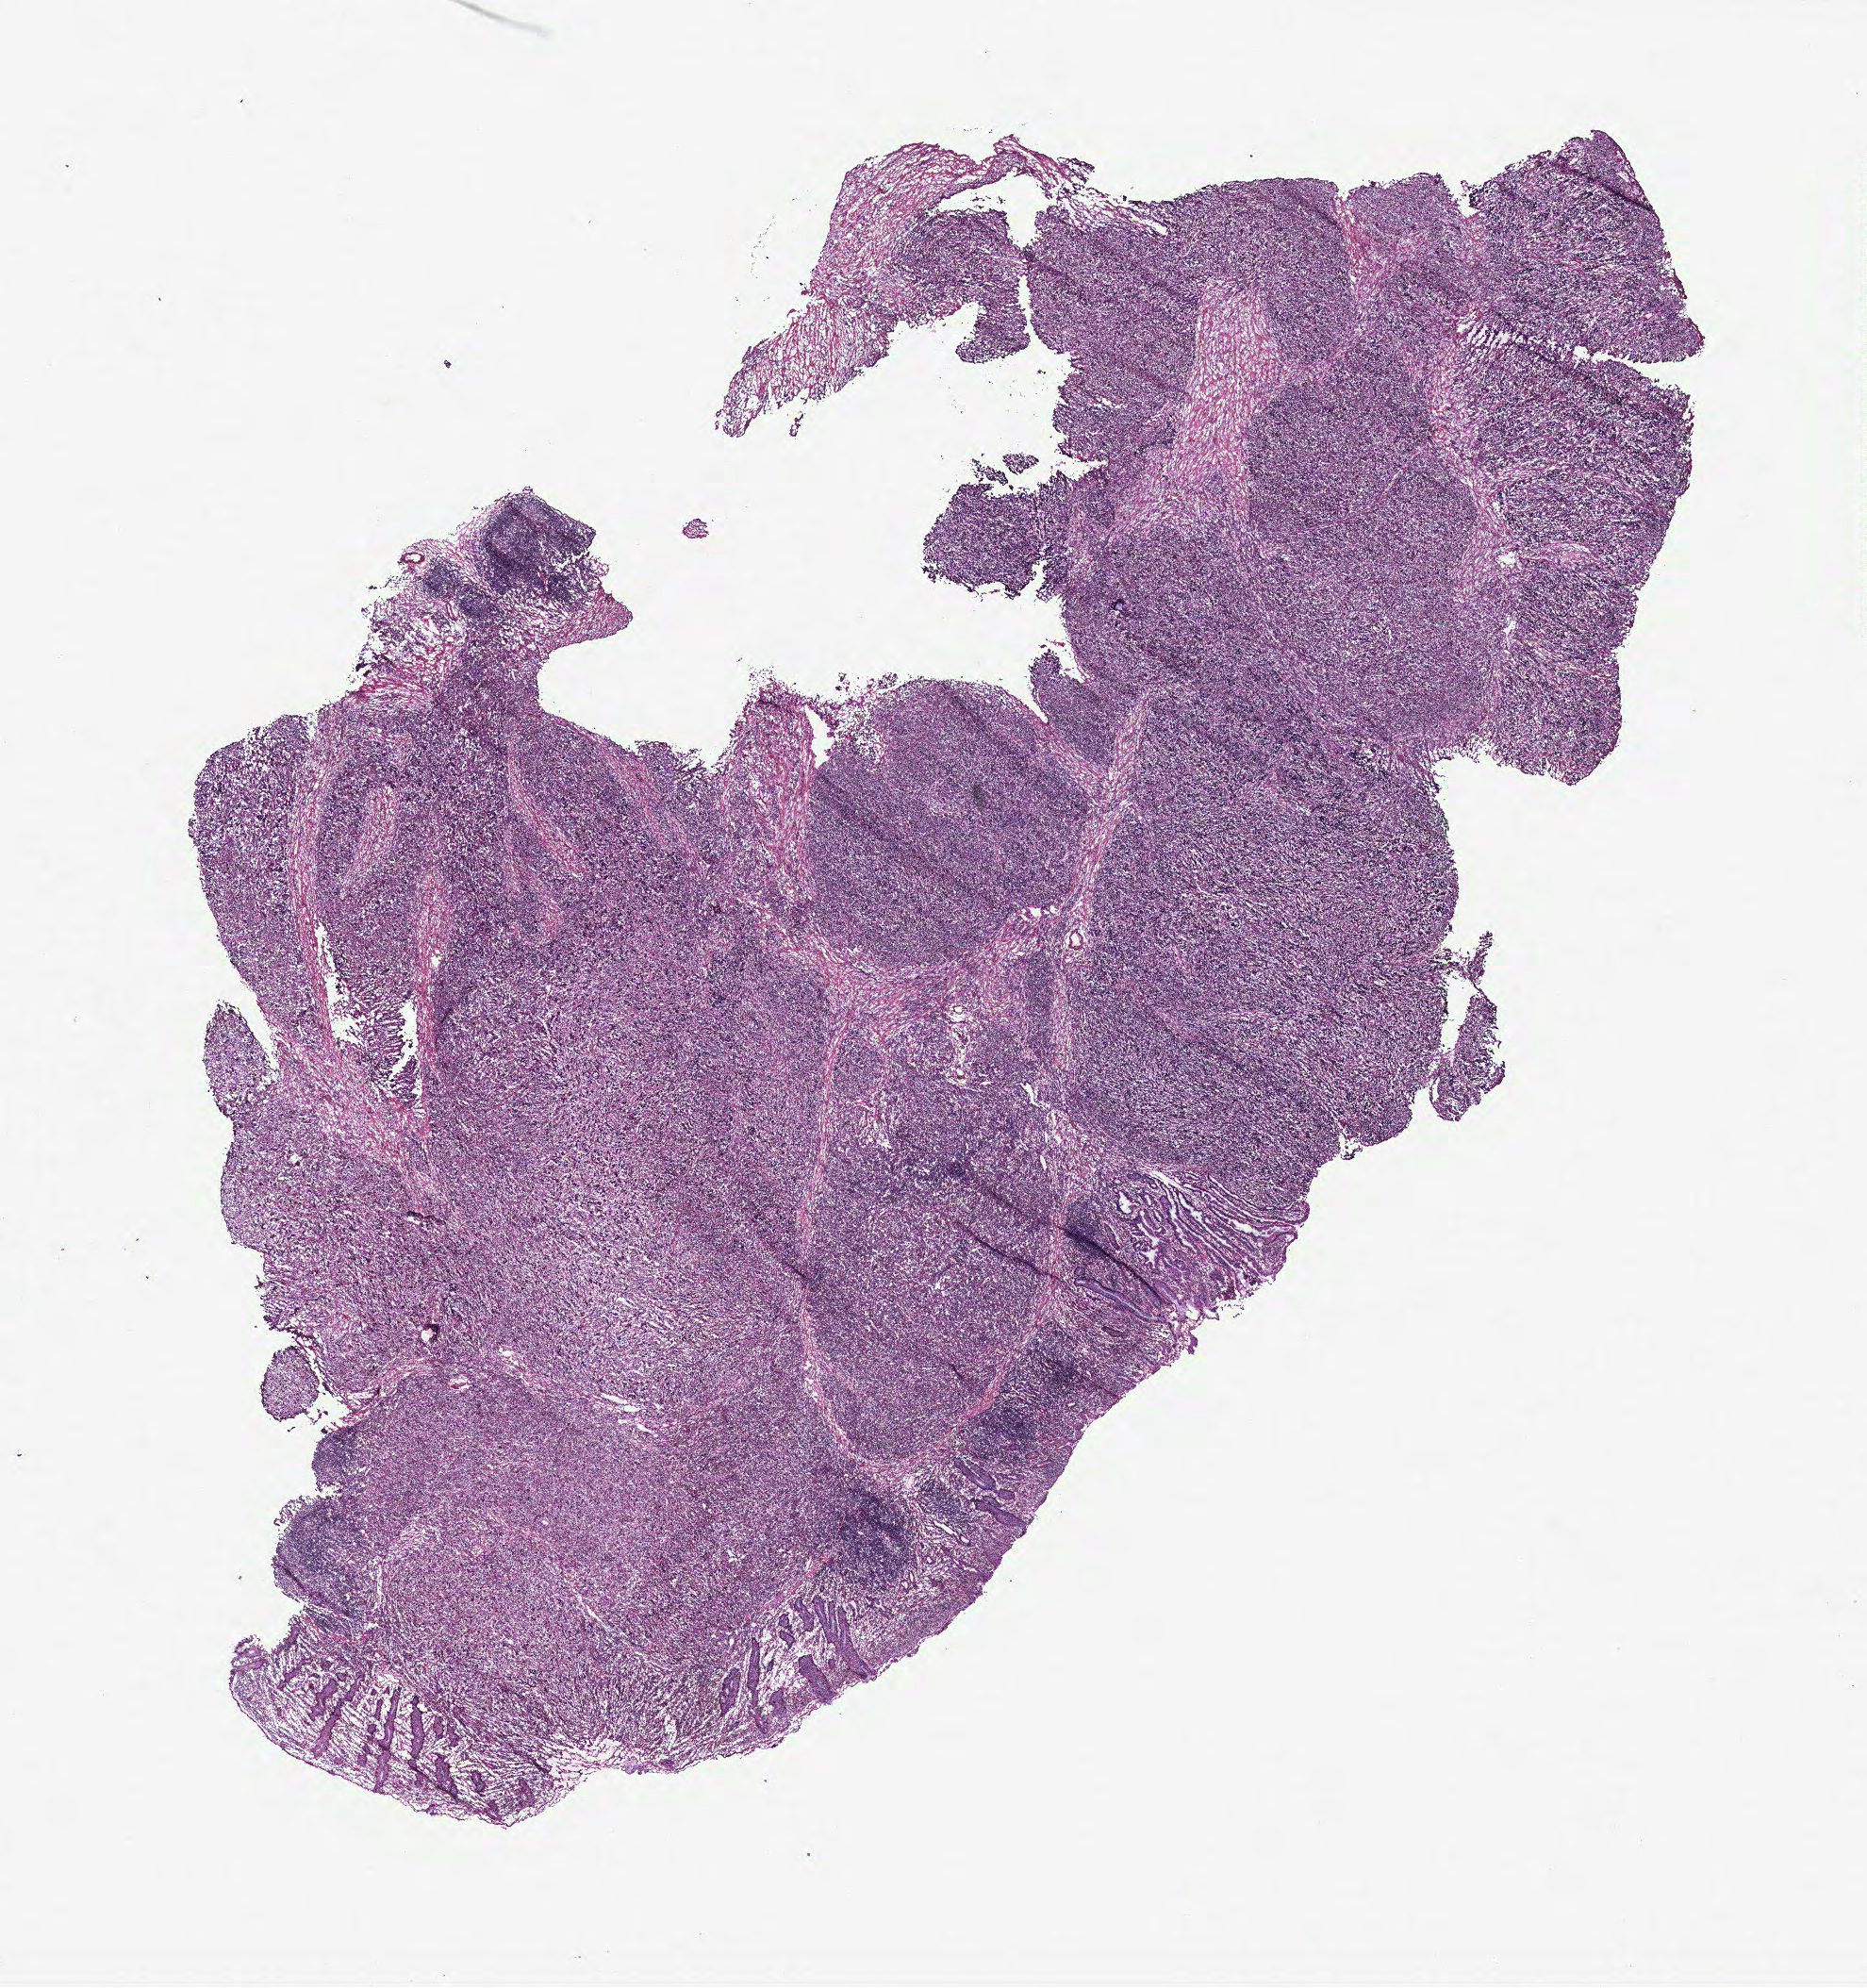
Whole-slide histology image, H&E-stained, shown as a low-resolution overview of the whole scanned area (about 15.8 x 16.9 mm), colon, tissue type not recorded.
• patient diagnosis (cohort enrolment): colon cancer (colon)